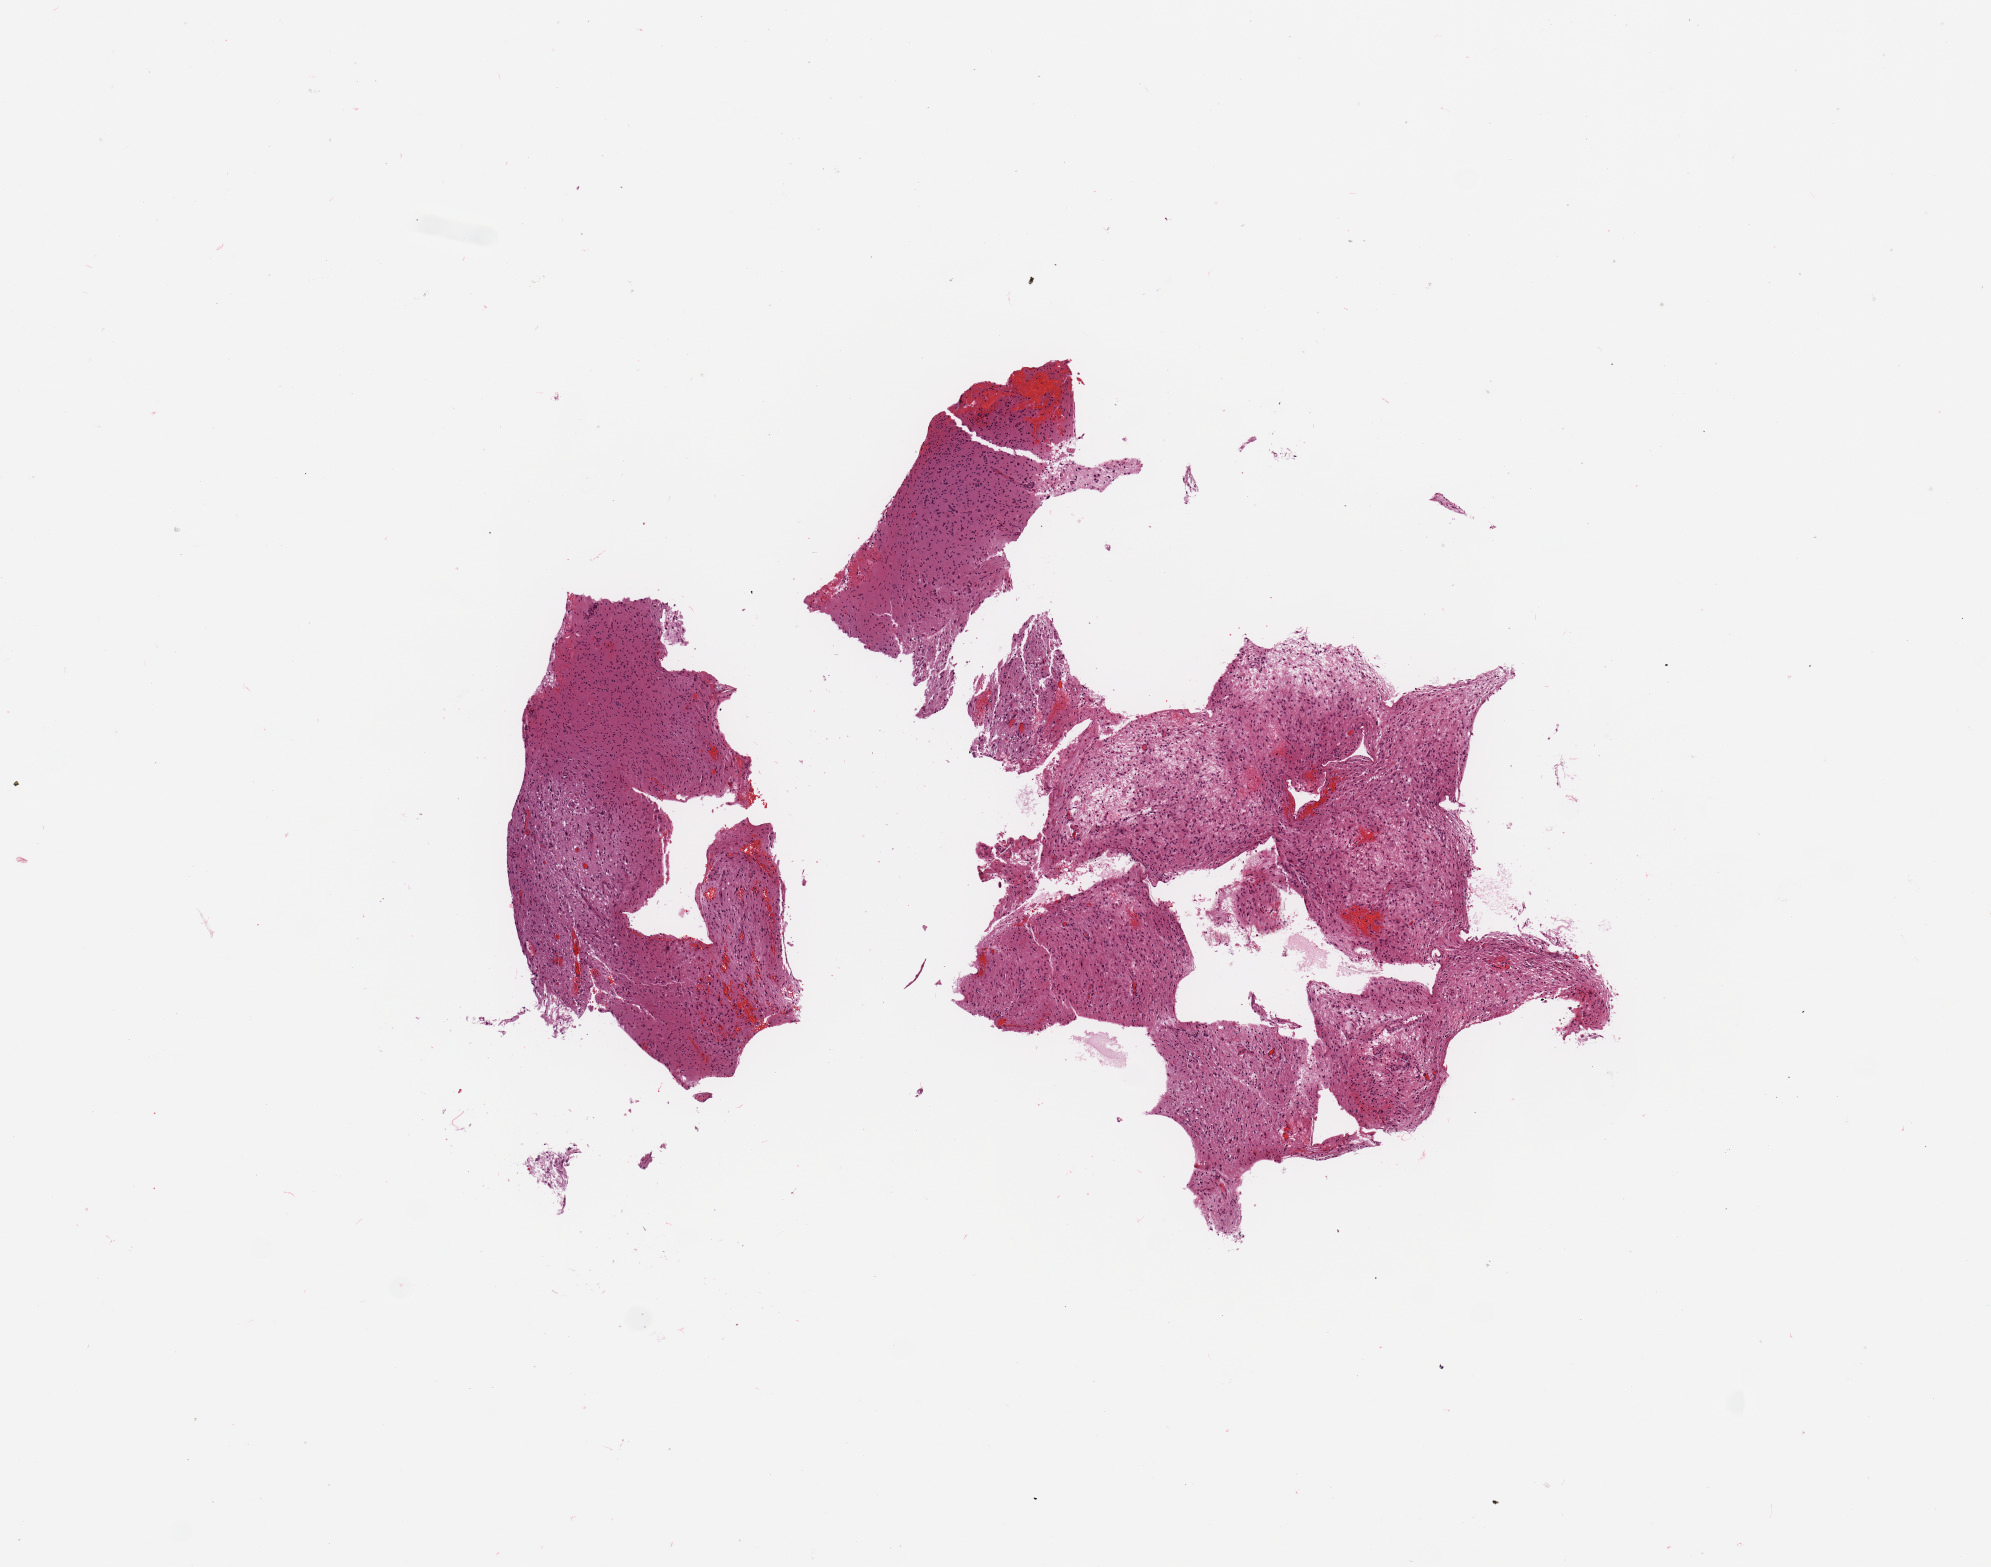
H&E-stained whole-slide image — a low-resolution overview of the entire scanned area, about 7.9 x 6.2 mm (slide scanned at 20x). Tumour tissue sample, sampled site: frontal lobe. Female, 80 y/o. Slide review estimates, as recorded: tumour nuclei 85%, necrosis 5%.
Diagnosis: Glioblastoma. Primary tumour site (as recorded): frontal lobe.